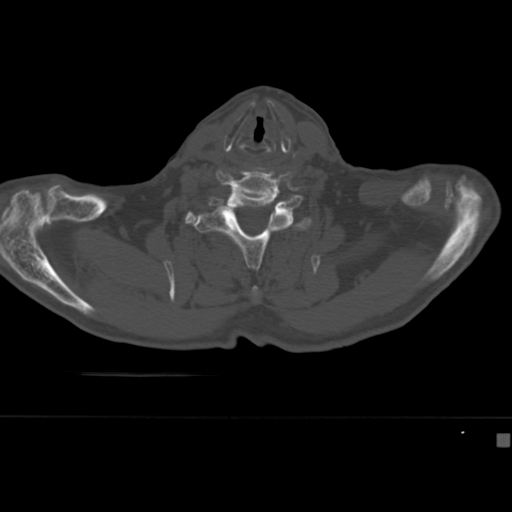
CT including the spine, one axial slice; slice 356 of 430 in the series (ordered by position); reconstruction kernel Br40s; 120 kVp; bone window (W 1800 / L 400 HU); 1.5 mm slice thickness; 512 × 512 image matrix. Patient: male, 64 years. Case-level facts recorded for this patient, not image findings: primary cancer: uterus; vertebrae with lytic lesions (as recorded): T1, T4, T5, T7, L5.
Outlined on this slice (semi-automatic segmentation, software-assisted and operator-edited):
- T2 vertebra: box from (x=251, y=285) to (x=261, y=304) px